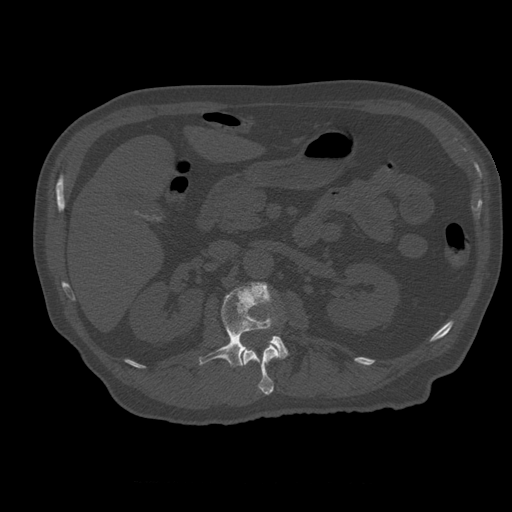
CT including the spine, one axial slice; slice 224 of 399 in the series (ordered by position); 120 kVp; bone window (W 1800 / L 400 HU); 1.25 mm slice thickness; 512 × 512 image matrix, field of view 407 × 407 mm. Patient age 73 years. From the clinical record (not read from this slice): primary cancer: prostate; vertebrae with lytic lesions (as recorded): L2.
Outlined on this slice (semi-automatic segmentation, software-assisted and operator-edited):
- L1 vertebra: bounding box [x1, y1, x2, y2] px = [241, 341, 281, 395]
- L2 vertebra: [199, 282, 289, 368]